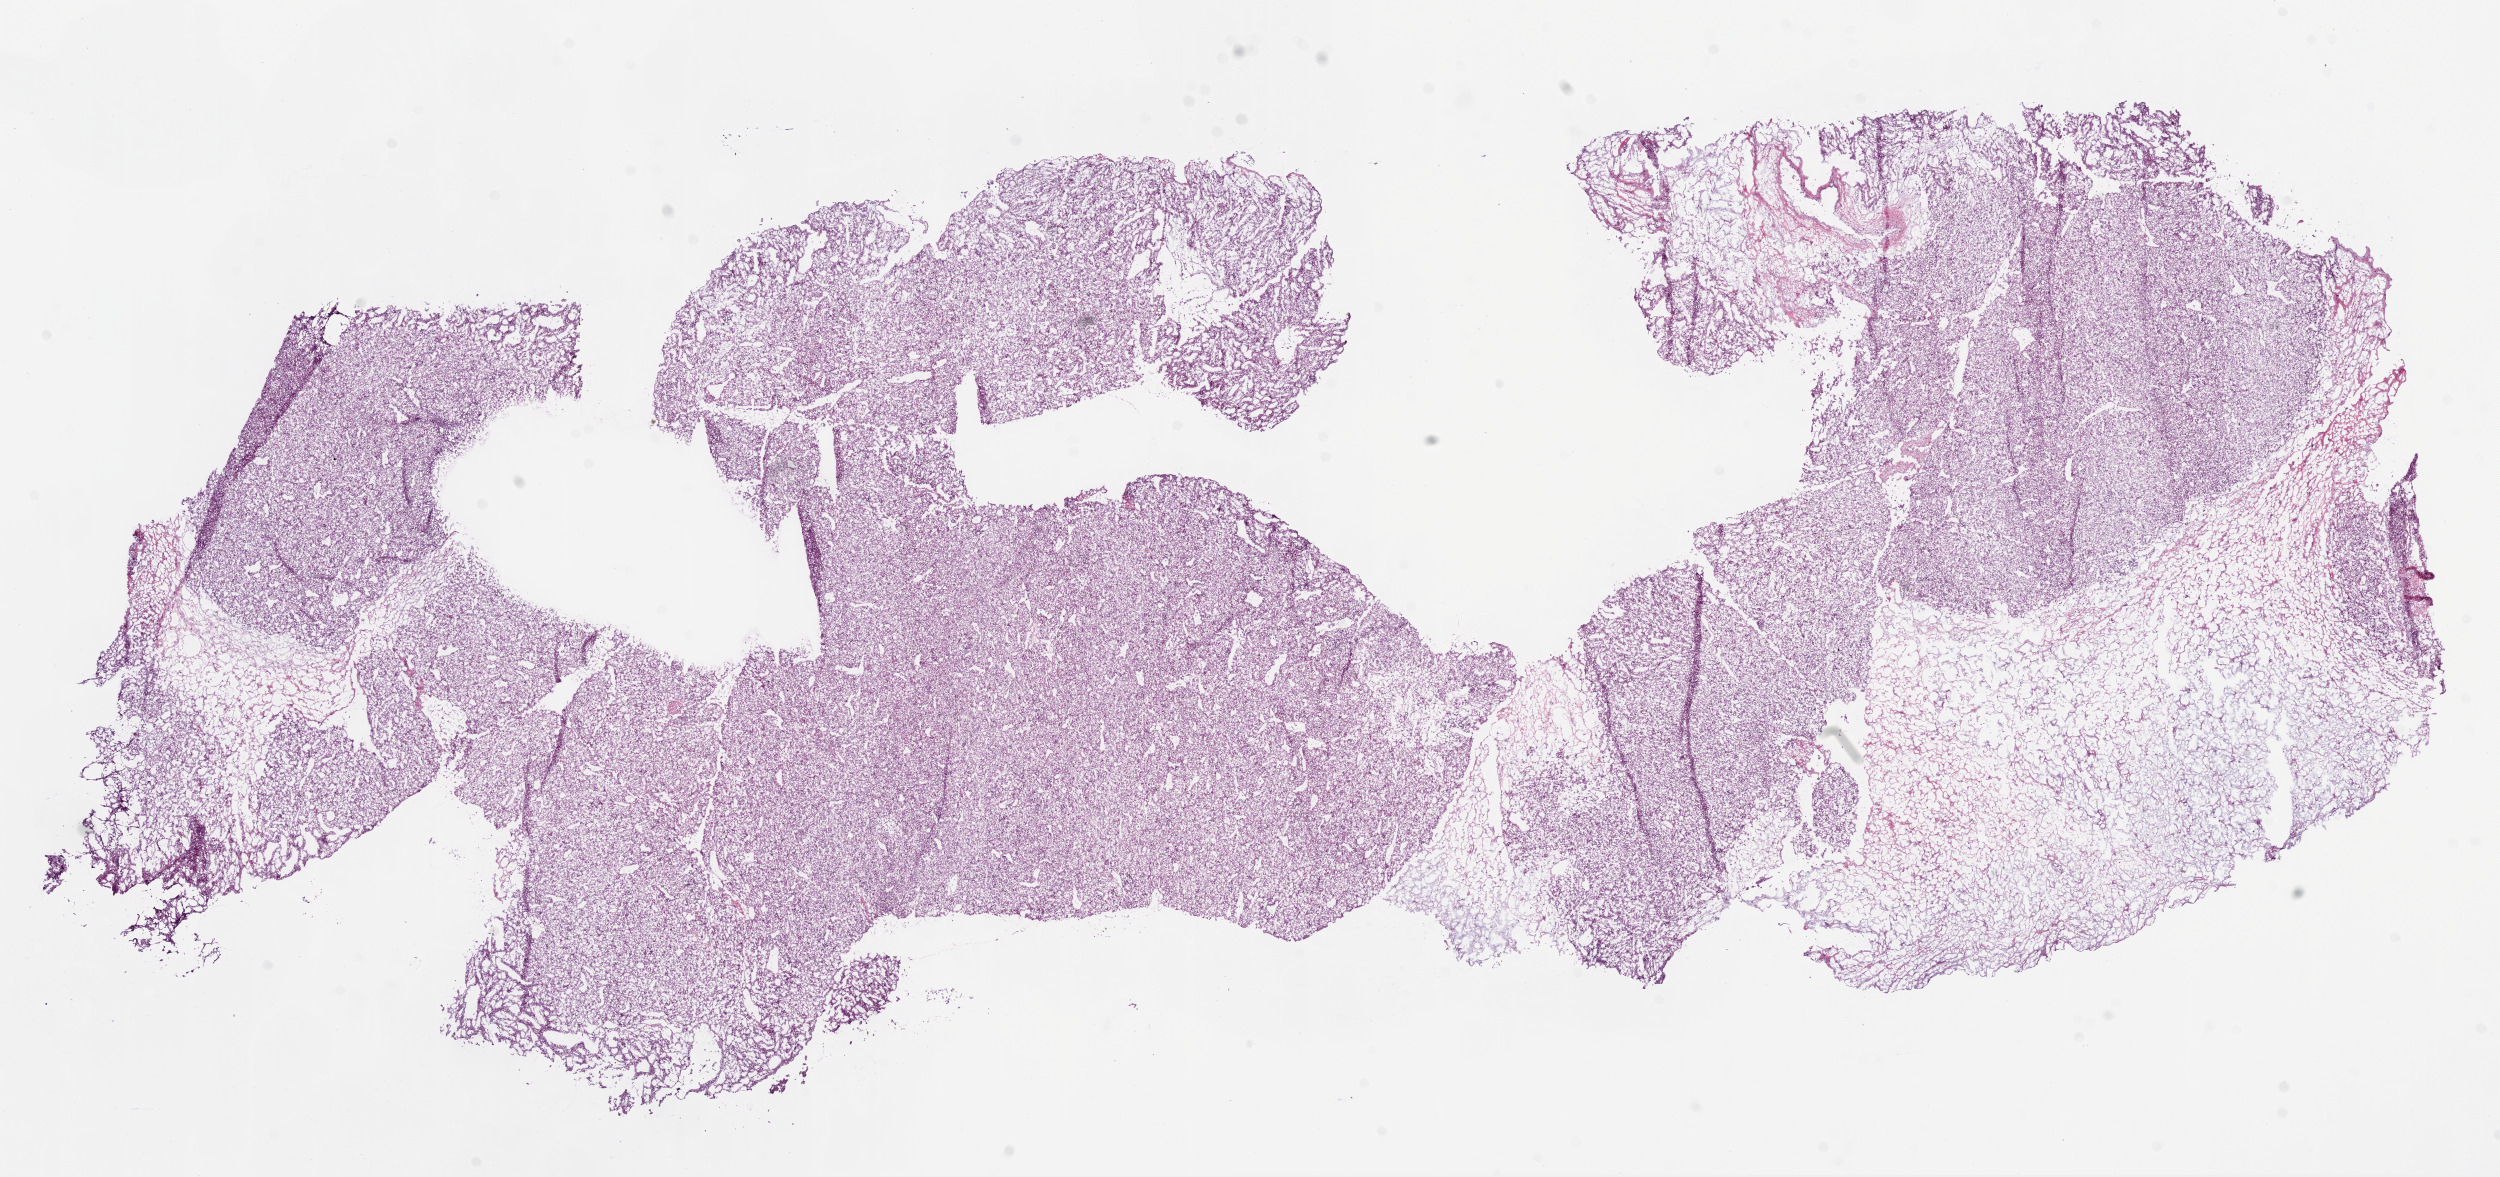
Whole-slide histology image, Hematoxylin and eosin (H&E) stained — low-resolution overview of the scanned area, about 20.1 x 9.4 mm (slide scanned at 20x); frozen section; sample: primary tumour, kidney. Patient: male, age at initial diagnosis 48 years. Histologic grade: G3 (poorly differentiated). Composition of this section per pathologist review: tumour cells 80%, tumour nuclei 85%, normal cells 0%, stromal cells 20%, necrosis 0%.
TNM: T3a NX M1. Diagnosis: Clear cell adenocarcinoma, NOS. AJCC pathologic stage: IV.